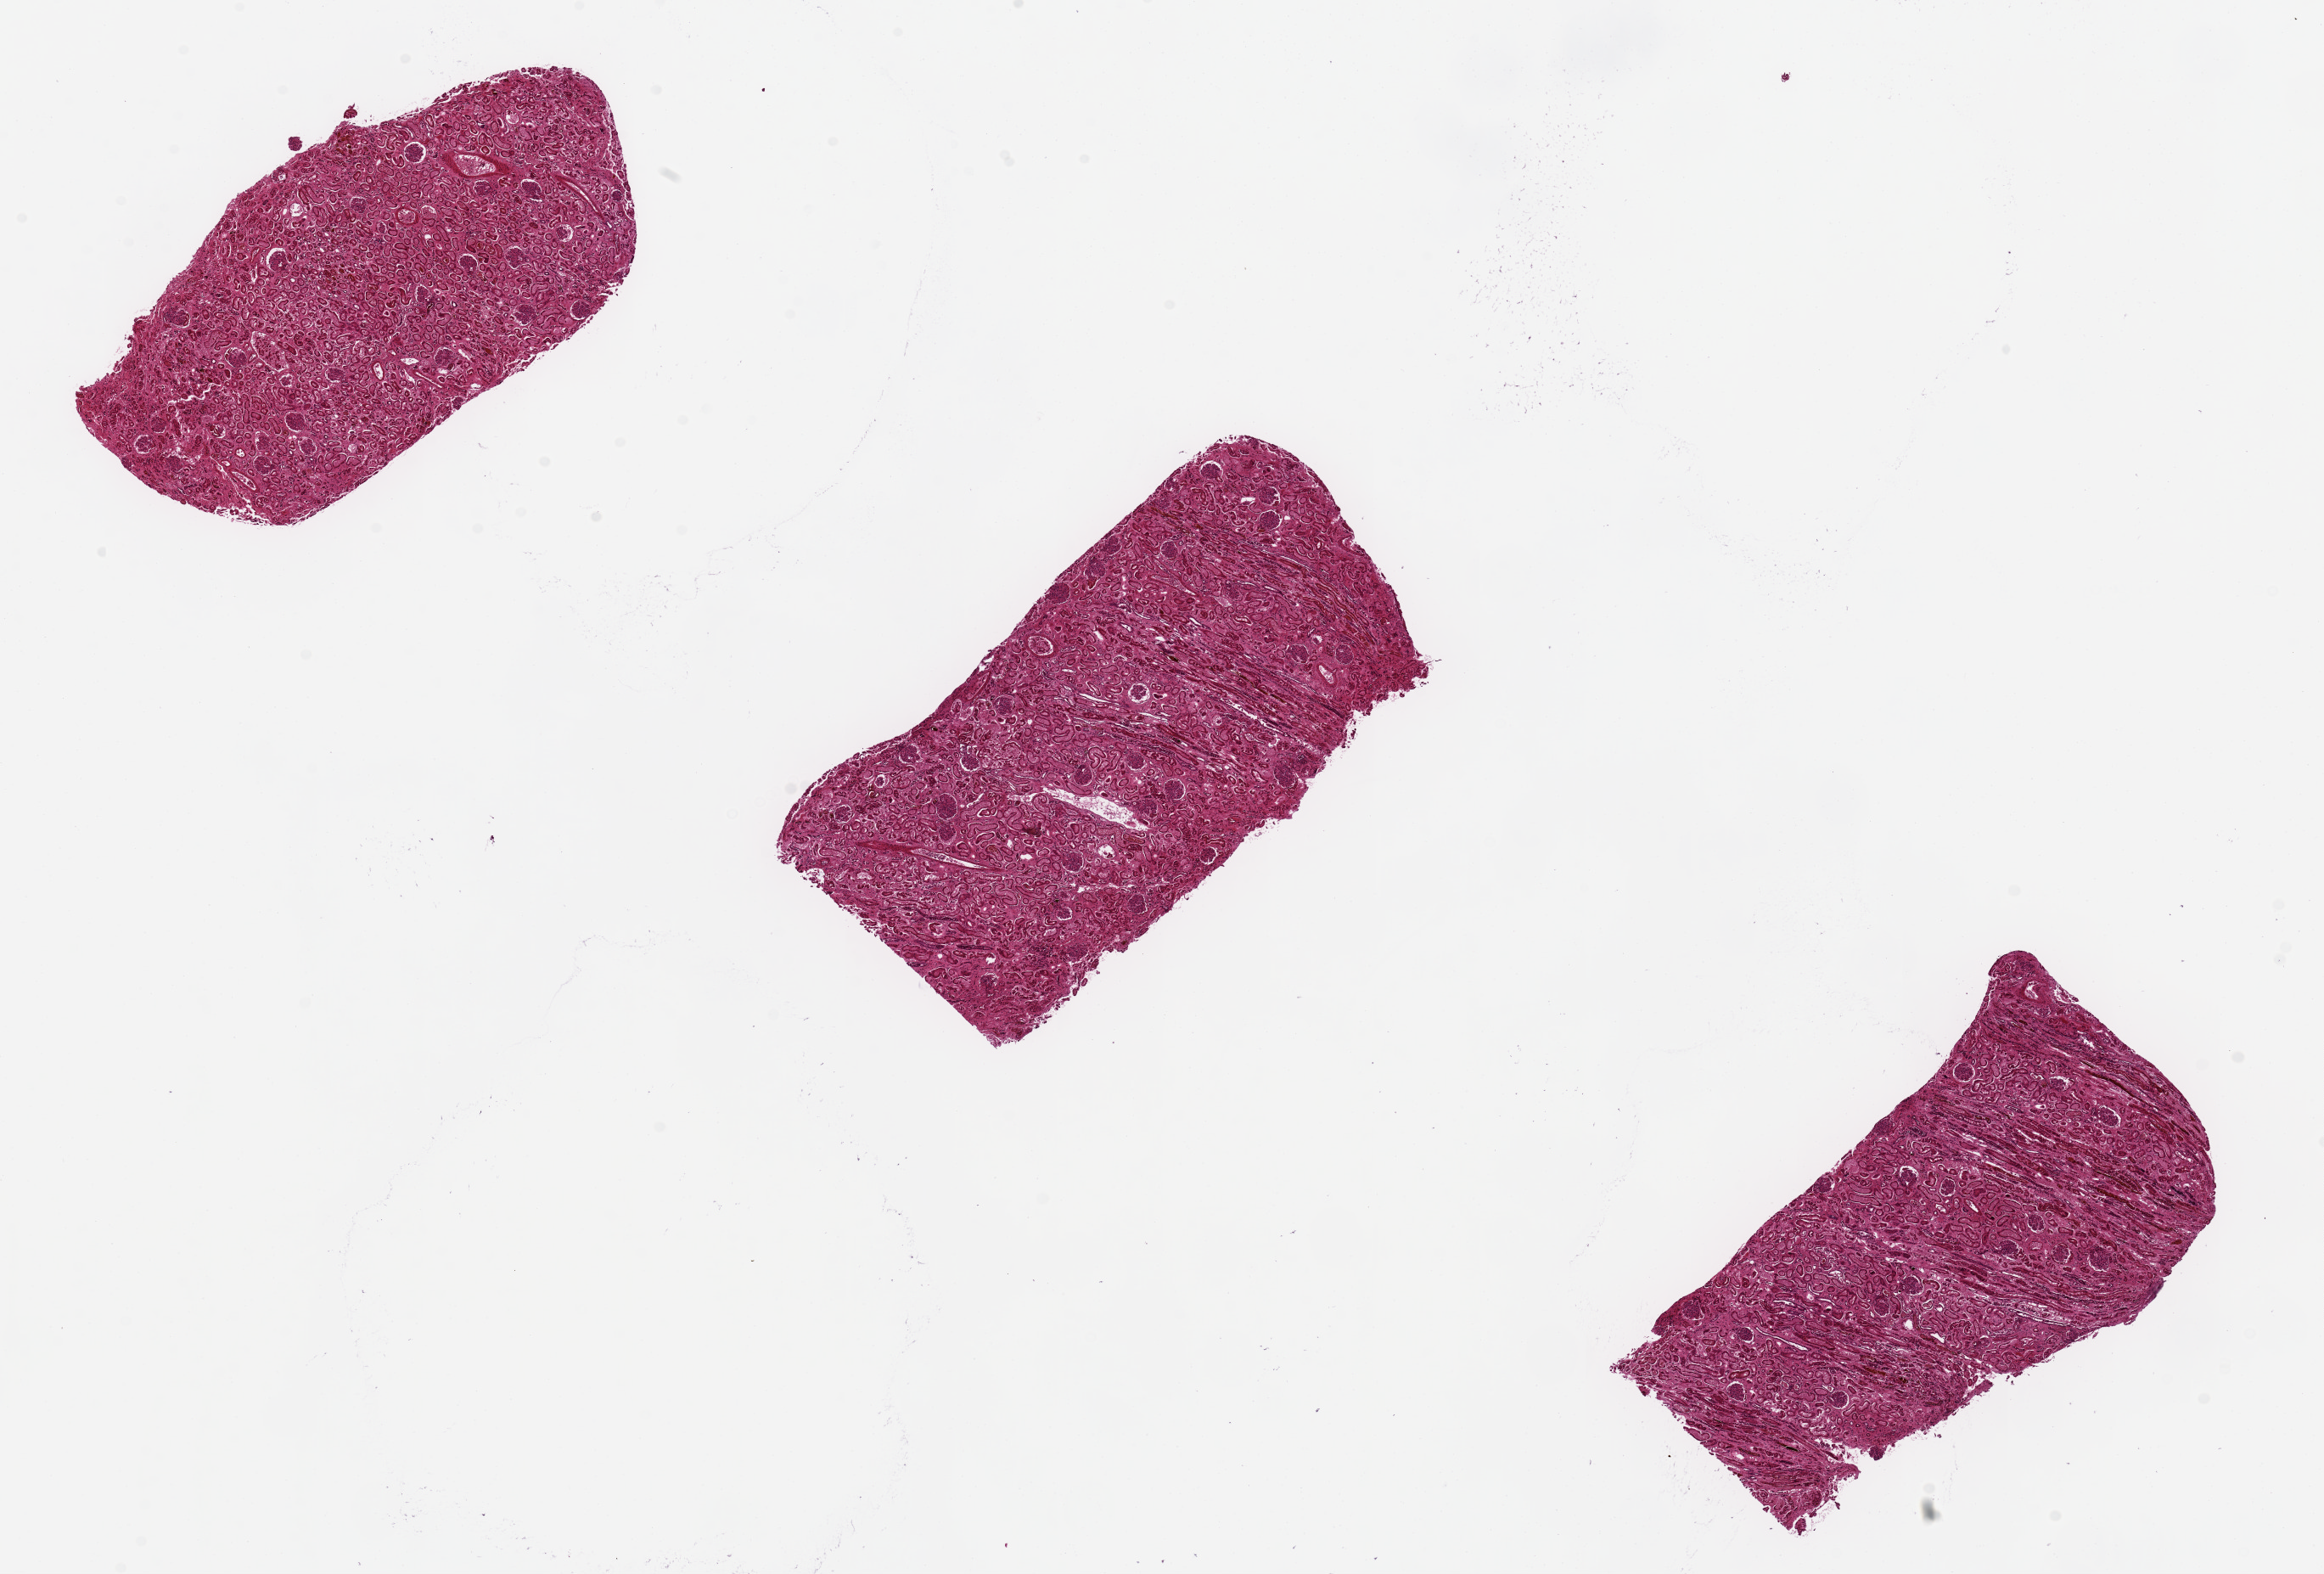
Haematoxylin and eosin whole-slide image — shown as a low-resolution overview of the whole scanned area (about 21.7 x 14.7 mm, from a 20x scan); PAXgene-fixed paraffin-embedded (PFPE) section; target tissue: renal cortex; tissue donor sample. Donor sex: male.
Review note (as recorded): 3 6x3mm pieces. Some red cell casts noted.